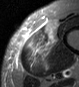
MRI of an extremity soft-tissue mass, one axial slice. STIR. MR volume resampled by the dataset authors to the PET/CT grid (not the native acquisition matrix). 3.27 mm slice thickness. 79 × 87 image matrix, field of view 77 × 85 mm. Male patient. From the clinical record (not read from this slice): histological type: pleiomorphic leiomyosarcoma; grade: high; site of the primary tumour: left thigh.
Annotated regions visible in this slice (expert contour drawn on MRI and transferred to this co-registered scan by the dataset authors):
- gross tumour volume including surrounding oedema: box from (x=24, y=20) to (x=58, y=72) px